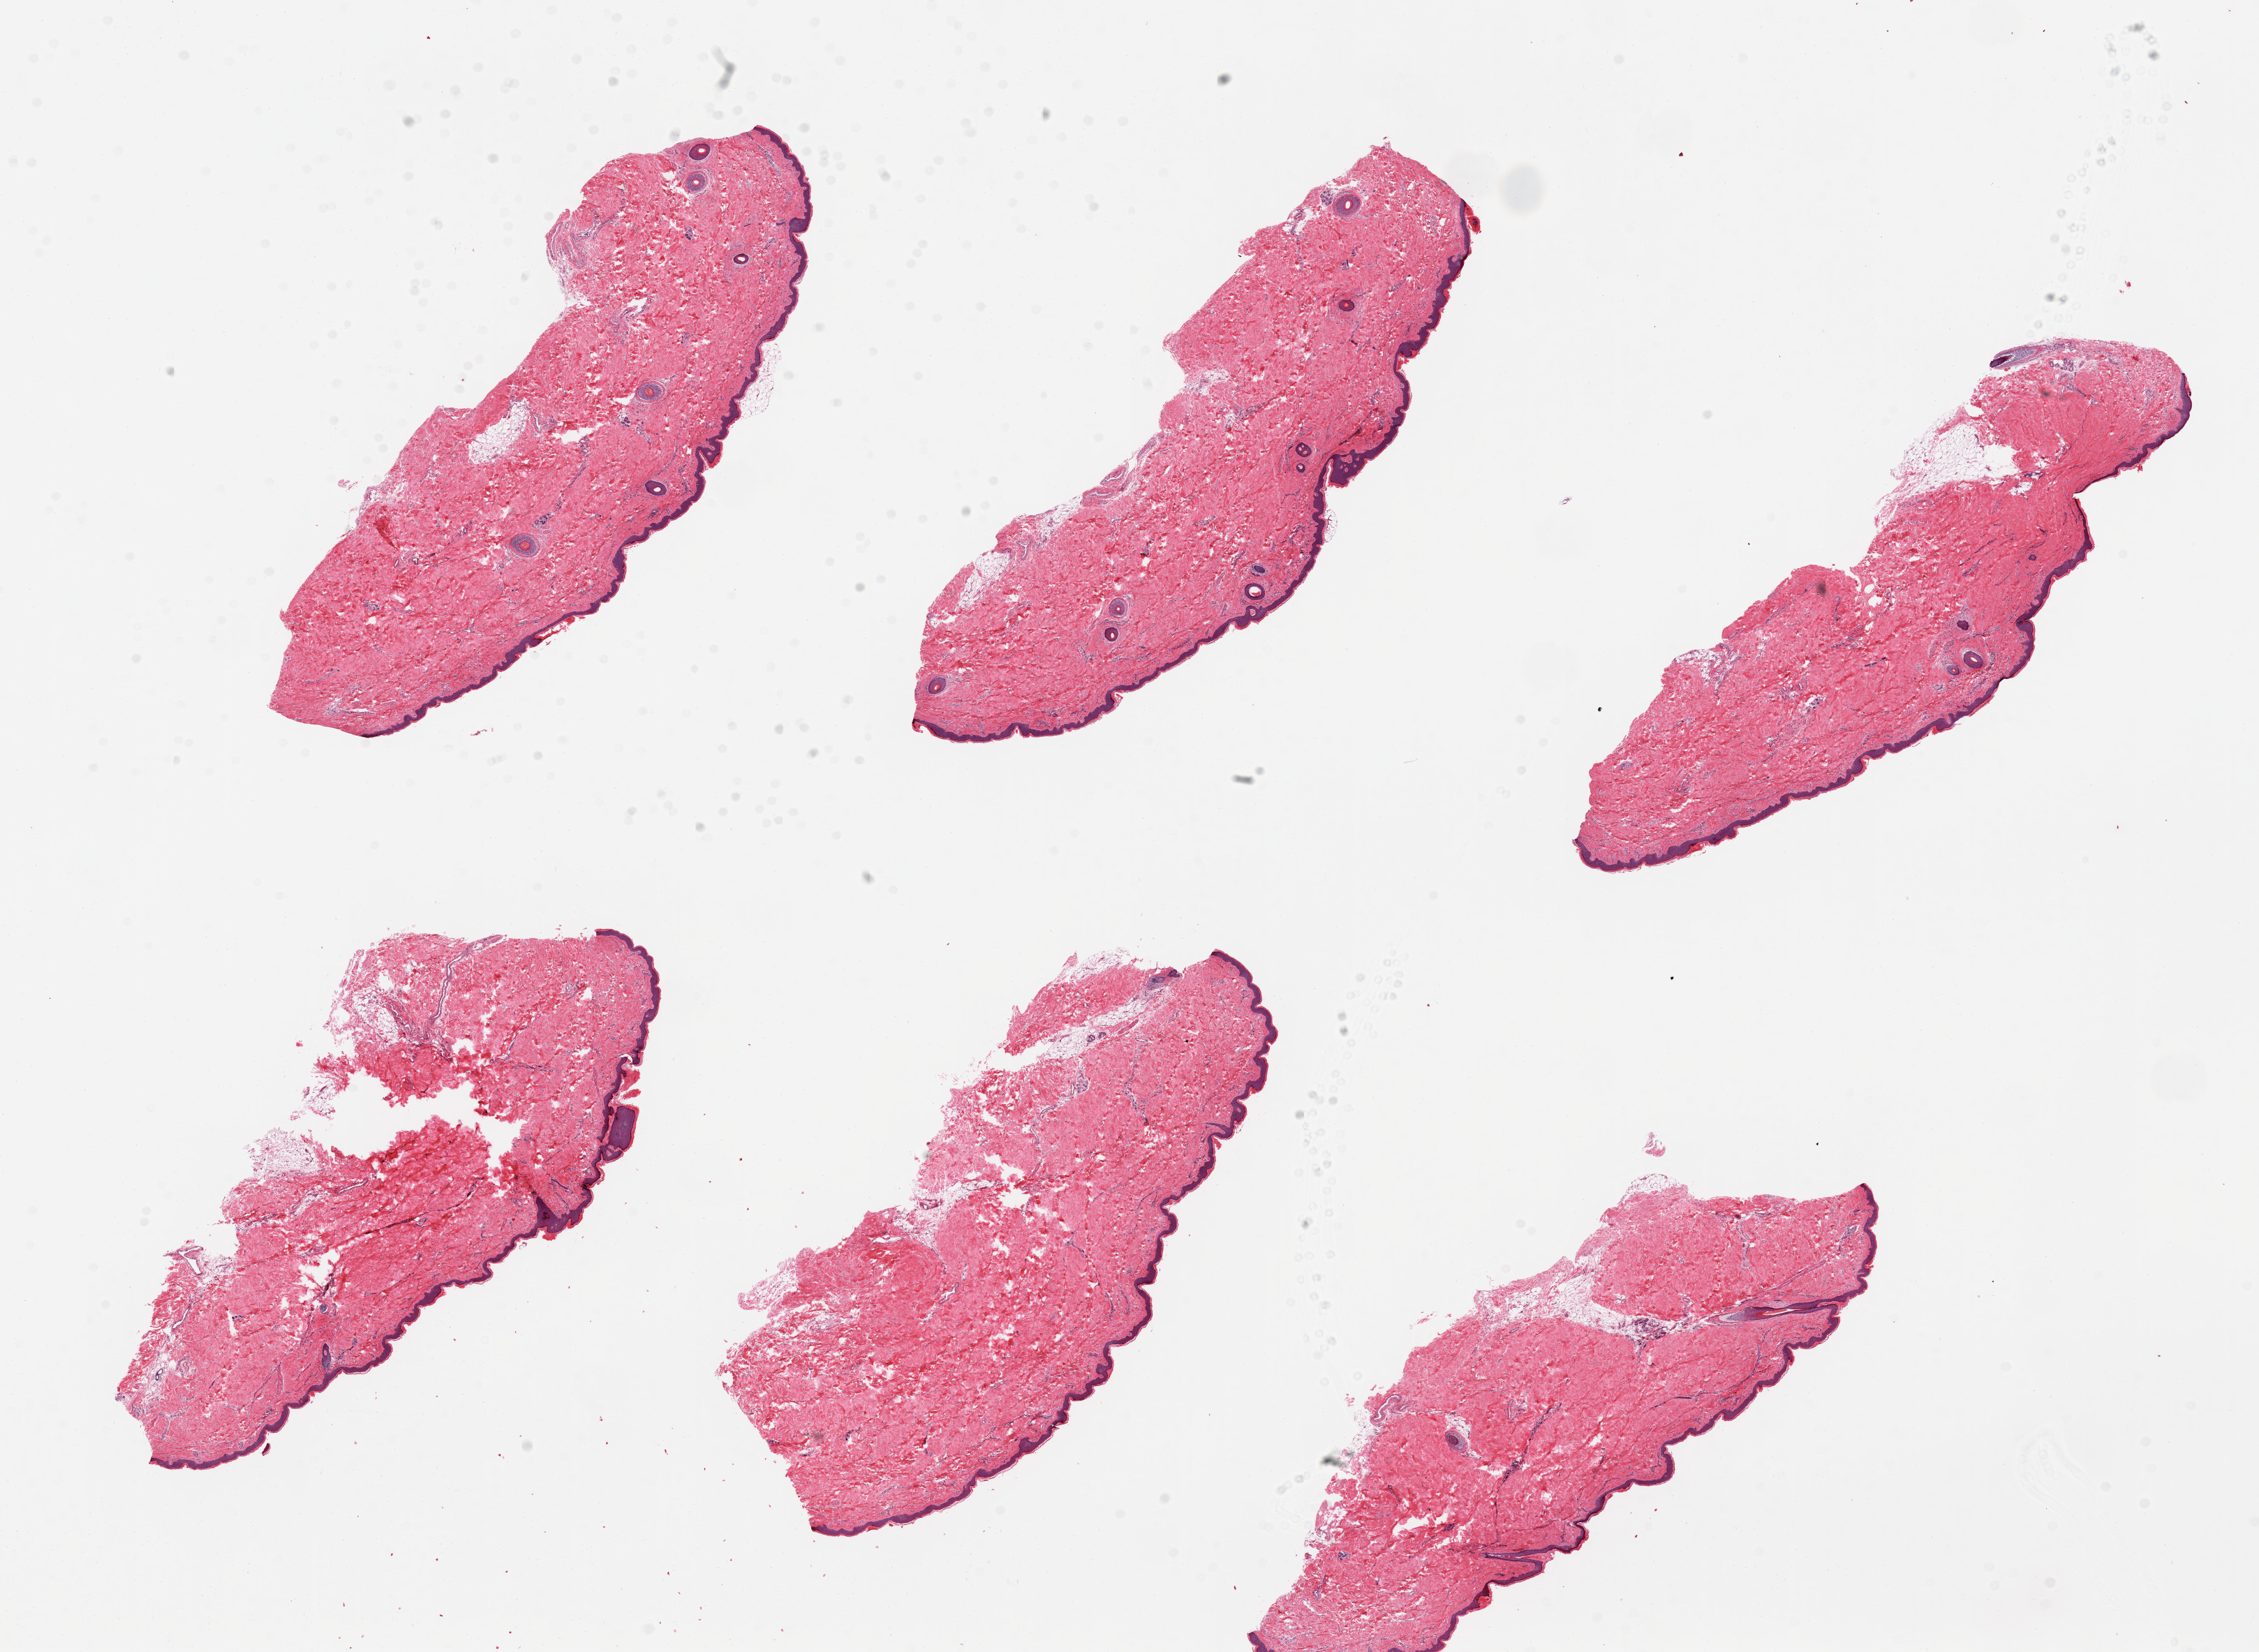
Digitized hematoxylin and eosin (H&E)-stained section — shown as a low-resolution overview of the whole scanned area (about 25.6 x 18.7 mm), PAXgene-fixed, paraffin-embedded tissue, sampled site (target tissue): skin of lower leg, donor tissue sample. Male donor.
Reviewer comment on this tissue sample: 6 pieces, well trimmed, squamous epithelium measures up to 70 microns.